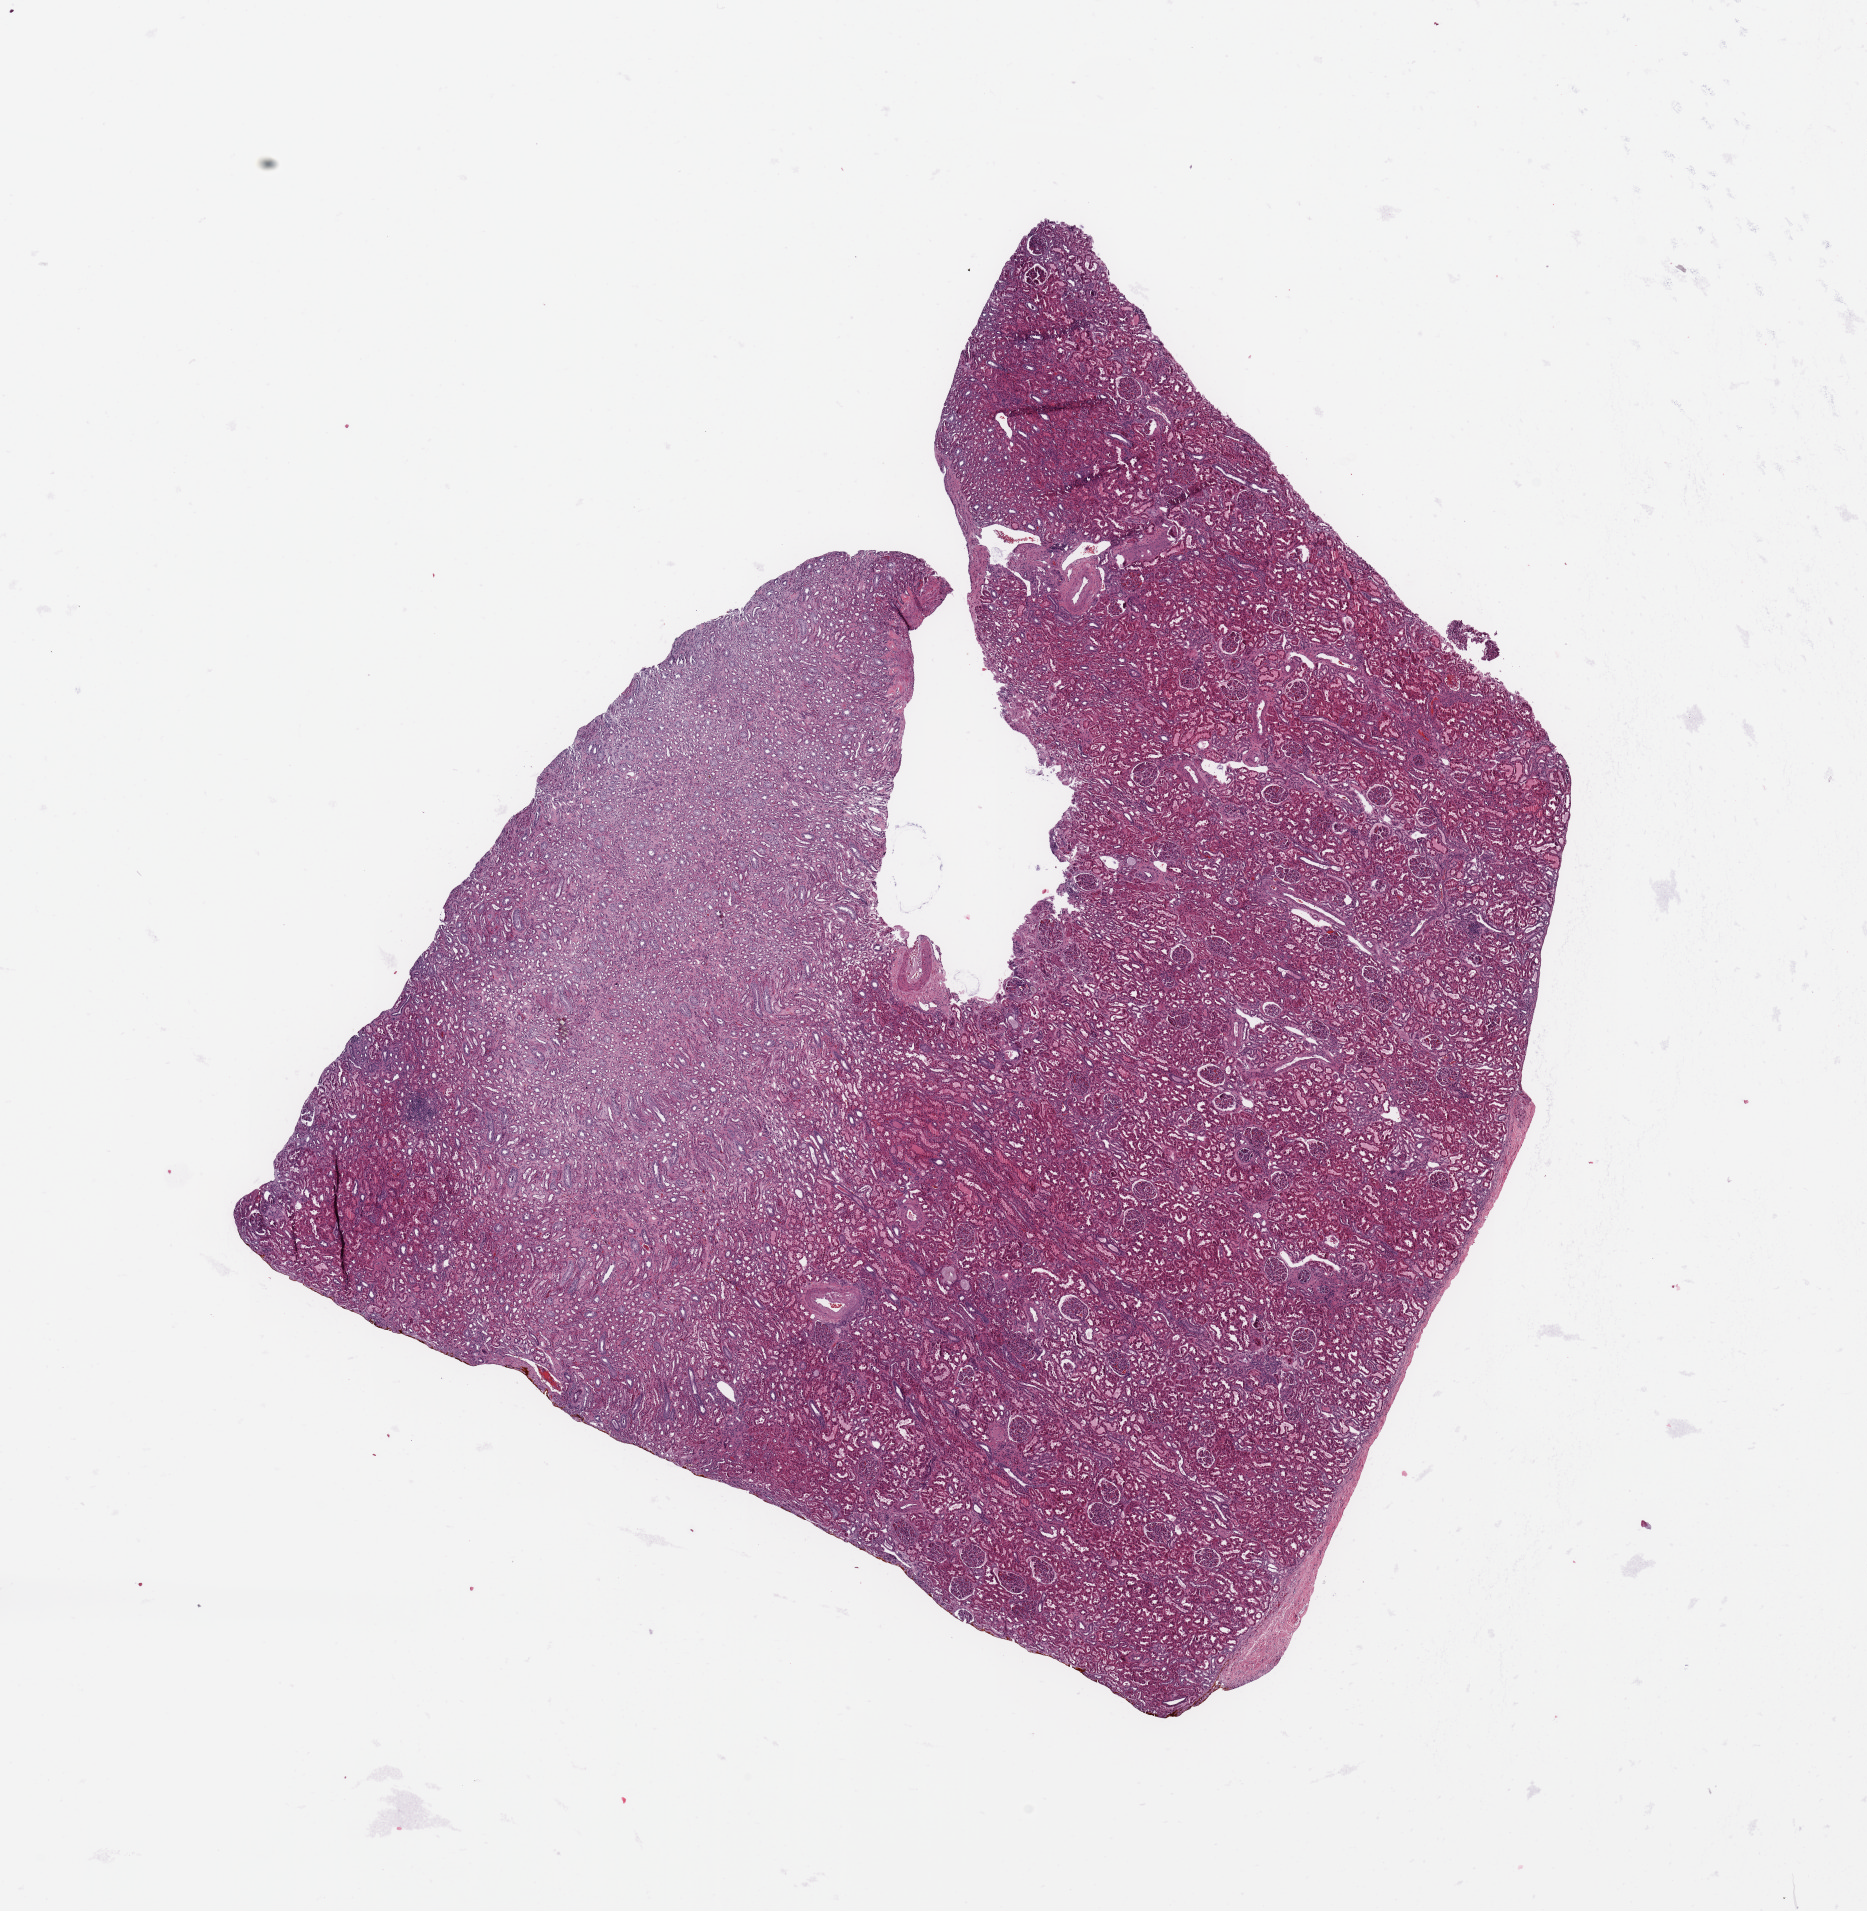
Digitized Hematoxylin and eosin (H&E) stained tissue section (whole slide), shown as a low-resolution overview of the whole scanned area (about 14.8 x 15.1 mm), normal (non-tumour) tissue sample, sampled site: kidney. 53-year-old male patient.
This section: normal (non-tumour) tissue from the same patient. Patient diagnosis: Renal cell carcinoma, NOS.